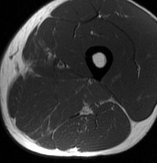
MRI of an extremity soft-tissue mass, one axial slice. Slice 30 of 70 in the series (ordered by position). MR volume resampled by the dataset authors to the PET/CT grid (not the native acquisition matrix). 3.27 mm slice thickness. 157 × 163 image matrix, field of view 153 × 159 mm. Male patient. From the clinical record (not read from this slice): histological type: extraskeletal osteosarcoma; grade: high; site of the primary tumour: left adductur.
Outlined on this slice (expert contour drawn on MRI and transferred to this co-registered scan by the dataset authors):
- gross tumour volume (mass): bounding box <17,72,112,132> (left, top, right, bottom; pixels)